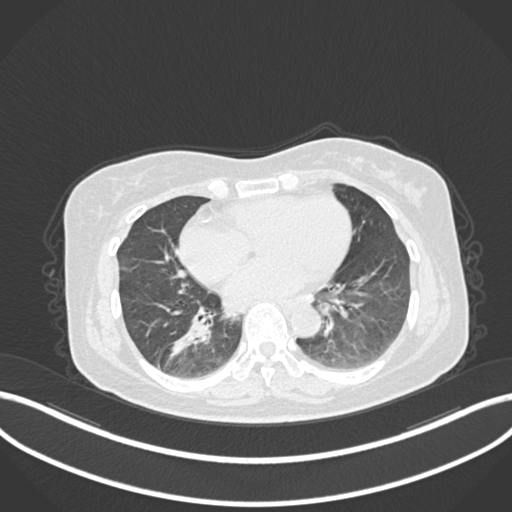
Chest CT, one axial slice. Slice 60 of 222 in the series (ordered by position). 120 kVp. Lung window (W 1500 / L -600 HU). 512 × 512 image matrix, field of view 400 × 400 mm. Female patient, age 67 years. From the clinical record (not read from this slice): clinical TNM (as recorded): T1c N1 M0.
Outlined on this slice (bounding box drawn by a radiologist):
- lung tumour (recorded histology: adenocarcinoma): bounding box (x1, y1, x2, y2) in pixels: (159, 296, 222, 368)